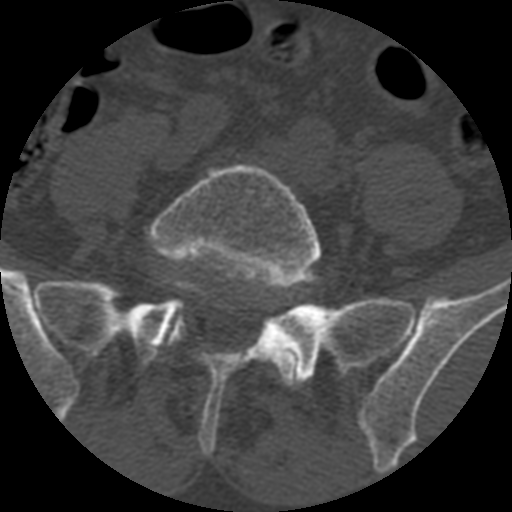
CT including the spine, one axial slice; slice 247 of 399 in the series (ordered by position); reconstruction kernel STANDARD; 120 kVp; bone window (W 1800 / L 400 HU); 1.25 mm slice thickness; 512 × 512 image matrix, field of view 160 × 160 mm. Patient age 71 years. Case-level facts recorded for this patient, not image findings: primary cancer: prostate.
Outlined on this slice (semi-automatically segmented with operator editing):
- L5 vertebra: bounding box <147,163,323,387> (left, top, right, bottom; pixels)